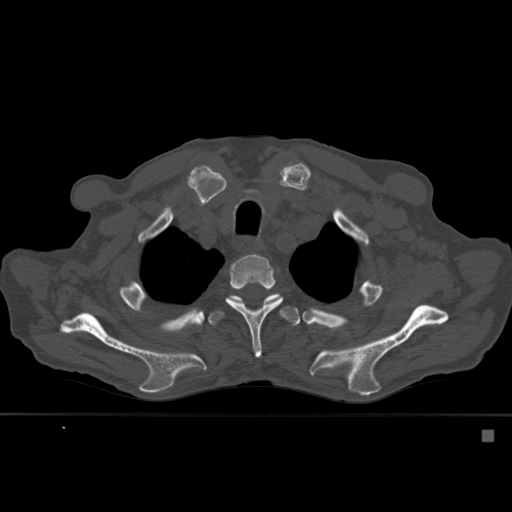
CT including the spine, one axial slice; bone window (W 1800 / L 400 HU); 1.5 mm slice thickness; 512 × 512 image matrix, field of view 373 × 373 mm. Patient: male, 78 years. Case-level facts recorded for this patient, not image findings: primary cancer: prostate.
Structures marked on this image (semi-automatically segmented with operator editing):
- T3 vertebra: bounding box <225,254,283,358> (left, top, right, bottom; pixels)
- T4 vertebra: <208,292,300,326>